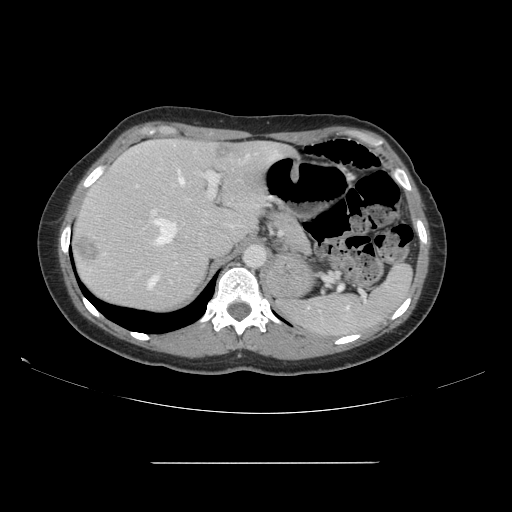
Contrast-enhanced abdominal CT, one axial slice. Position 112 of 151 along the scan axis. 120 kVp. Soft-tissue window (W 400 / L 40 HU). 512 × 512 image matrix, field of view 421 × 421 mm. Female patient, age 46 years. Case-level facts recorded for this patient, not image findings: diagnosis: colorectal cancer liver metastases, imaged before liver resection; multiple liver metastases: yes.
Annotated regions visible in this slice (outlined manually by an expert reader):
- hepatic veins: bounding box [x1, y1, x2, y2] px = [153, 154, 251, 246]
- liver: [72, 140, 290, 312]
- planned liver remnant (the part of the liver to remain after resection): [88, 140, 289, 252]
- portal vein (with intrahepatic branches): [136, 171, 218, 289]
- liver metastasis: [76, 235, 101, 264]
- liver metastasis: [214, 145, 232, 160]